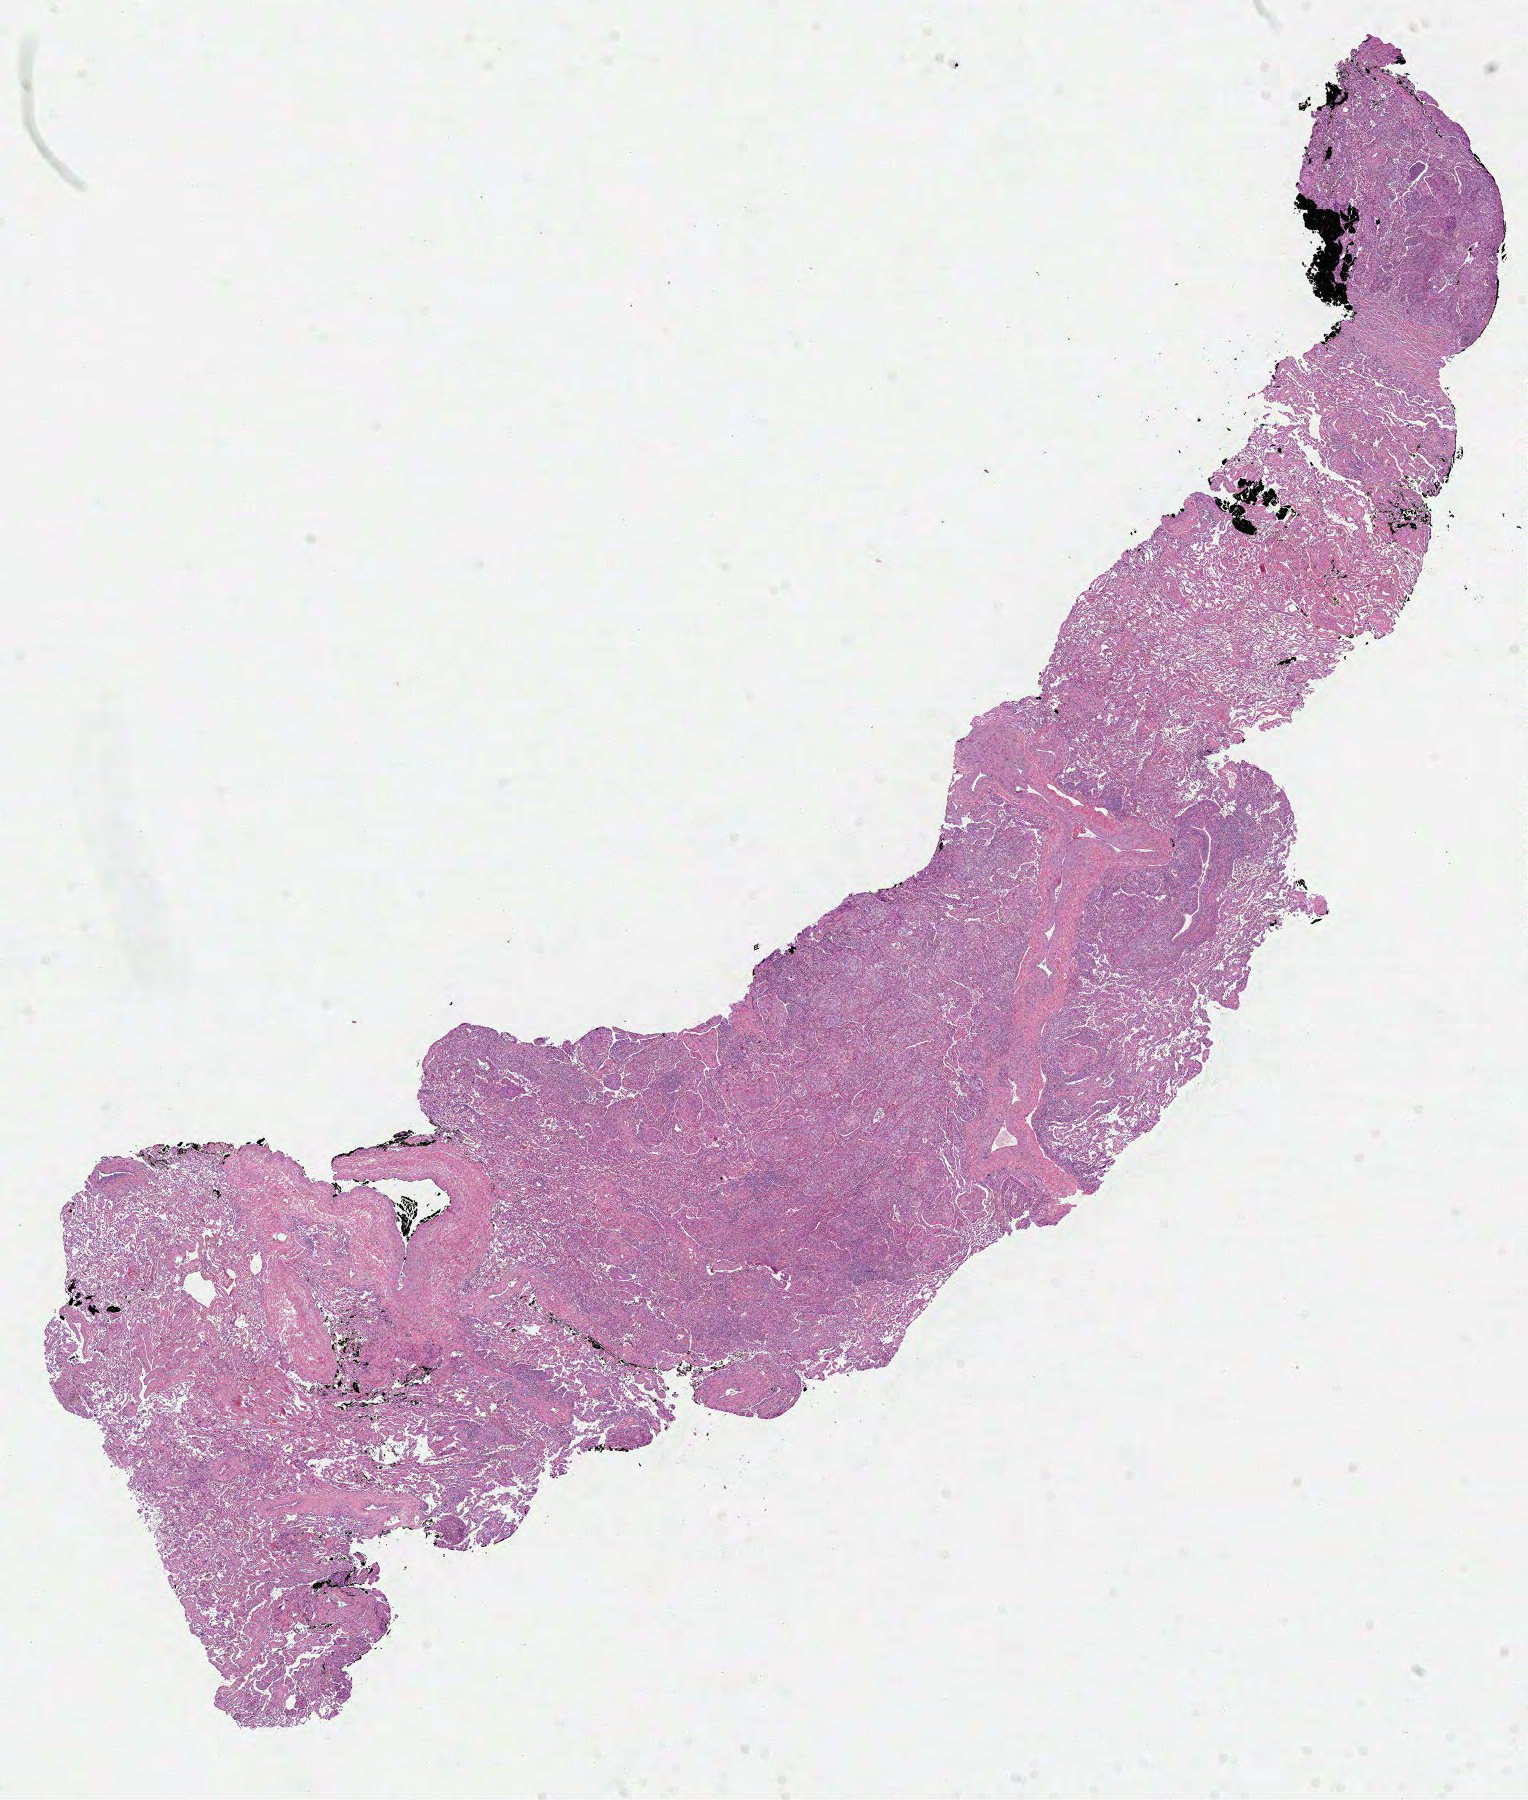
Digitized Hematoxylin and eosin (H&E) stained tissue section (whole slide), shown as a low-resolution overview of the whole scanned area (about 12.3 x 14.5 mm); FFPE section; sample: primary tumour, lung. Female patient; age at initial diagnosis 66 years.
* histologic diagnosis: Squamous cell carcinoma, NOS
* AJCC pathologic stage: IB